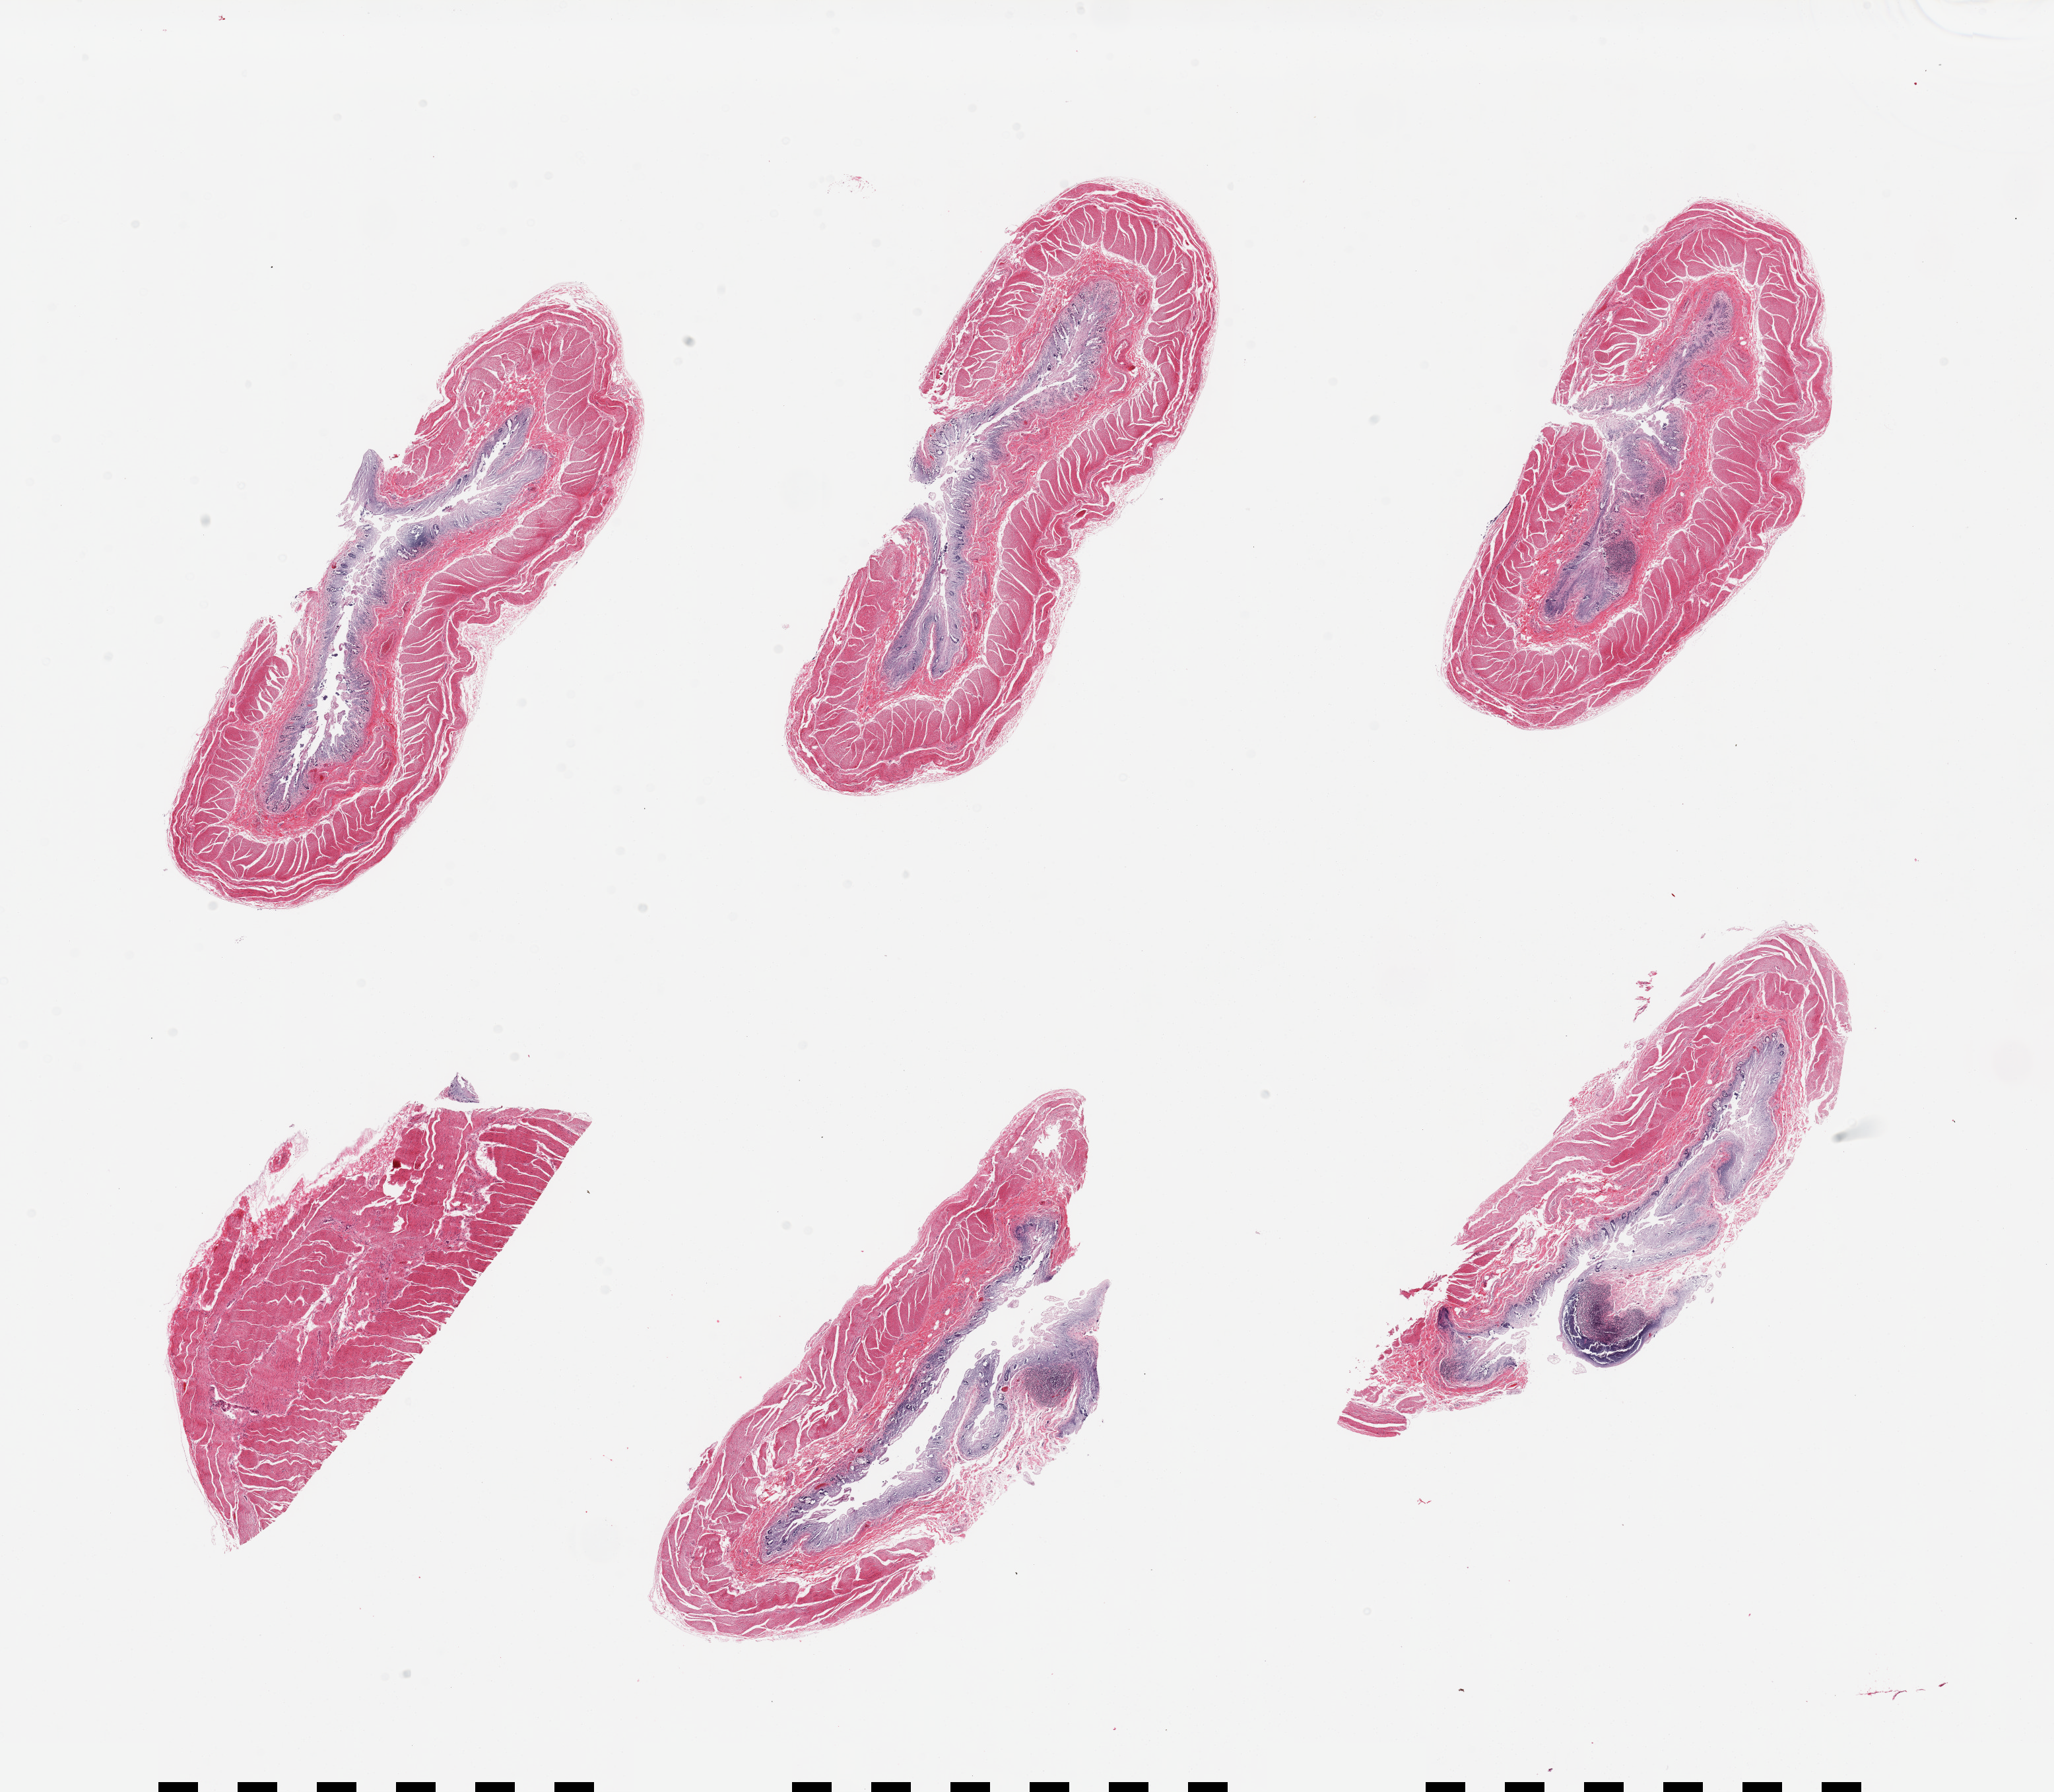
Digitized haematoxylin and eosin-stained section — whole scanned area (about 24.6 x 21.5 mm, slide scanned at 20x) shown as a low-resolution overview, PAXgene-fixed, paraffin-embedded tissue, sampled site (target tissue): ileum, donor tissue sample. Donor sex: male.
Reviewer comment on this tissue sample: 6 pieces; all include muscularis (not target), 5 contain mucosa; mucosa/lymphoid tissue severely autolyzed.